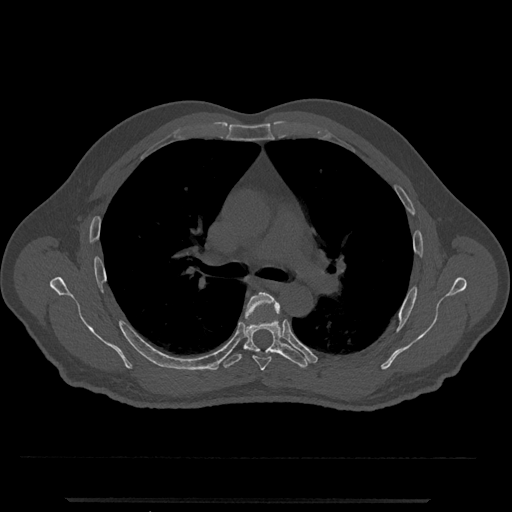
CT including the spine, one axial slice. Position 763 of 797 along the scan axis. Bone window (W 1800 / L 400 HU). 0.5 mm slice thickness. 512 × 512 image matrix. Male patient, age 63 years. From the clinical record (not read from this slice): primary cancer: prostate.
Outlined on this slice (semi-automatic segmentation, software-assisted and operator-edited):
- T5 vertebra: box from (x=245, y=292) to (x=280, y=371) px
- T6 vertebra: (x=223, y=305)–(x=309, y=369)